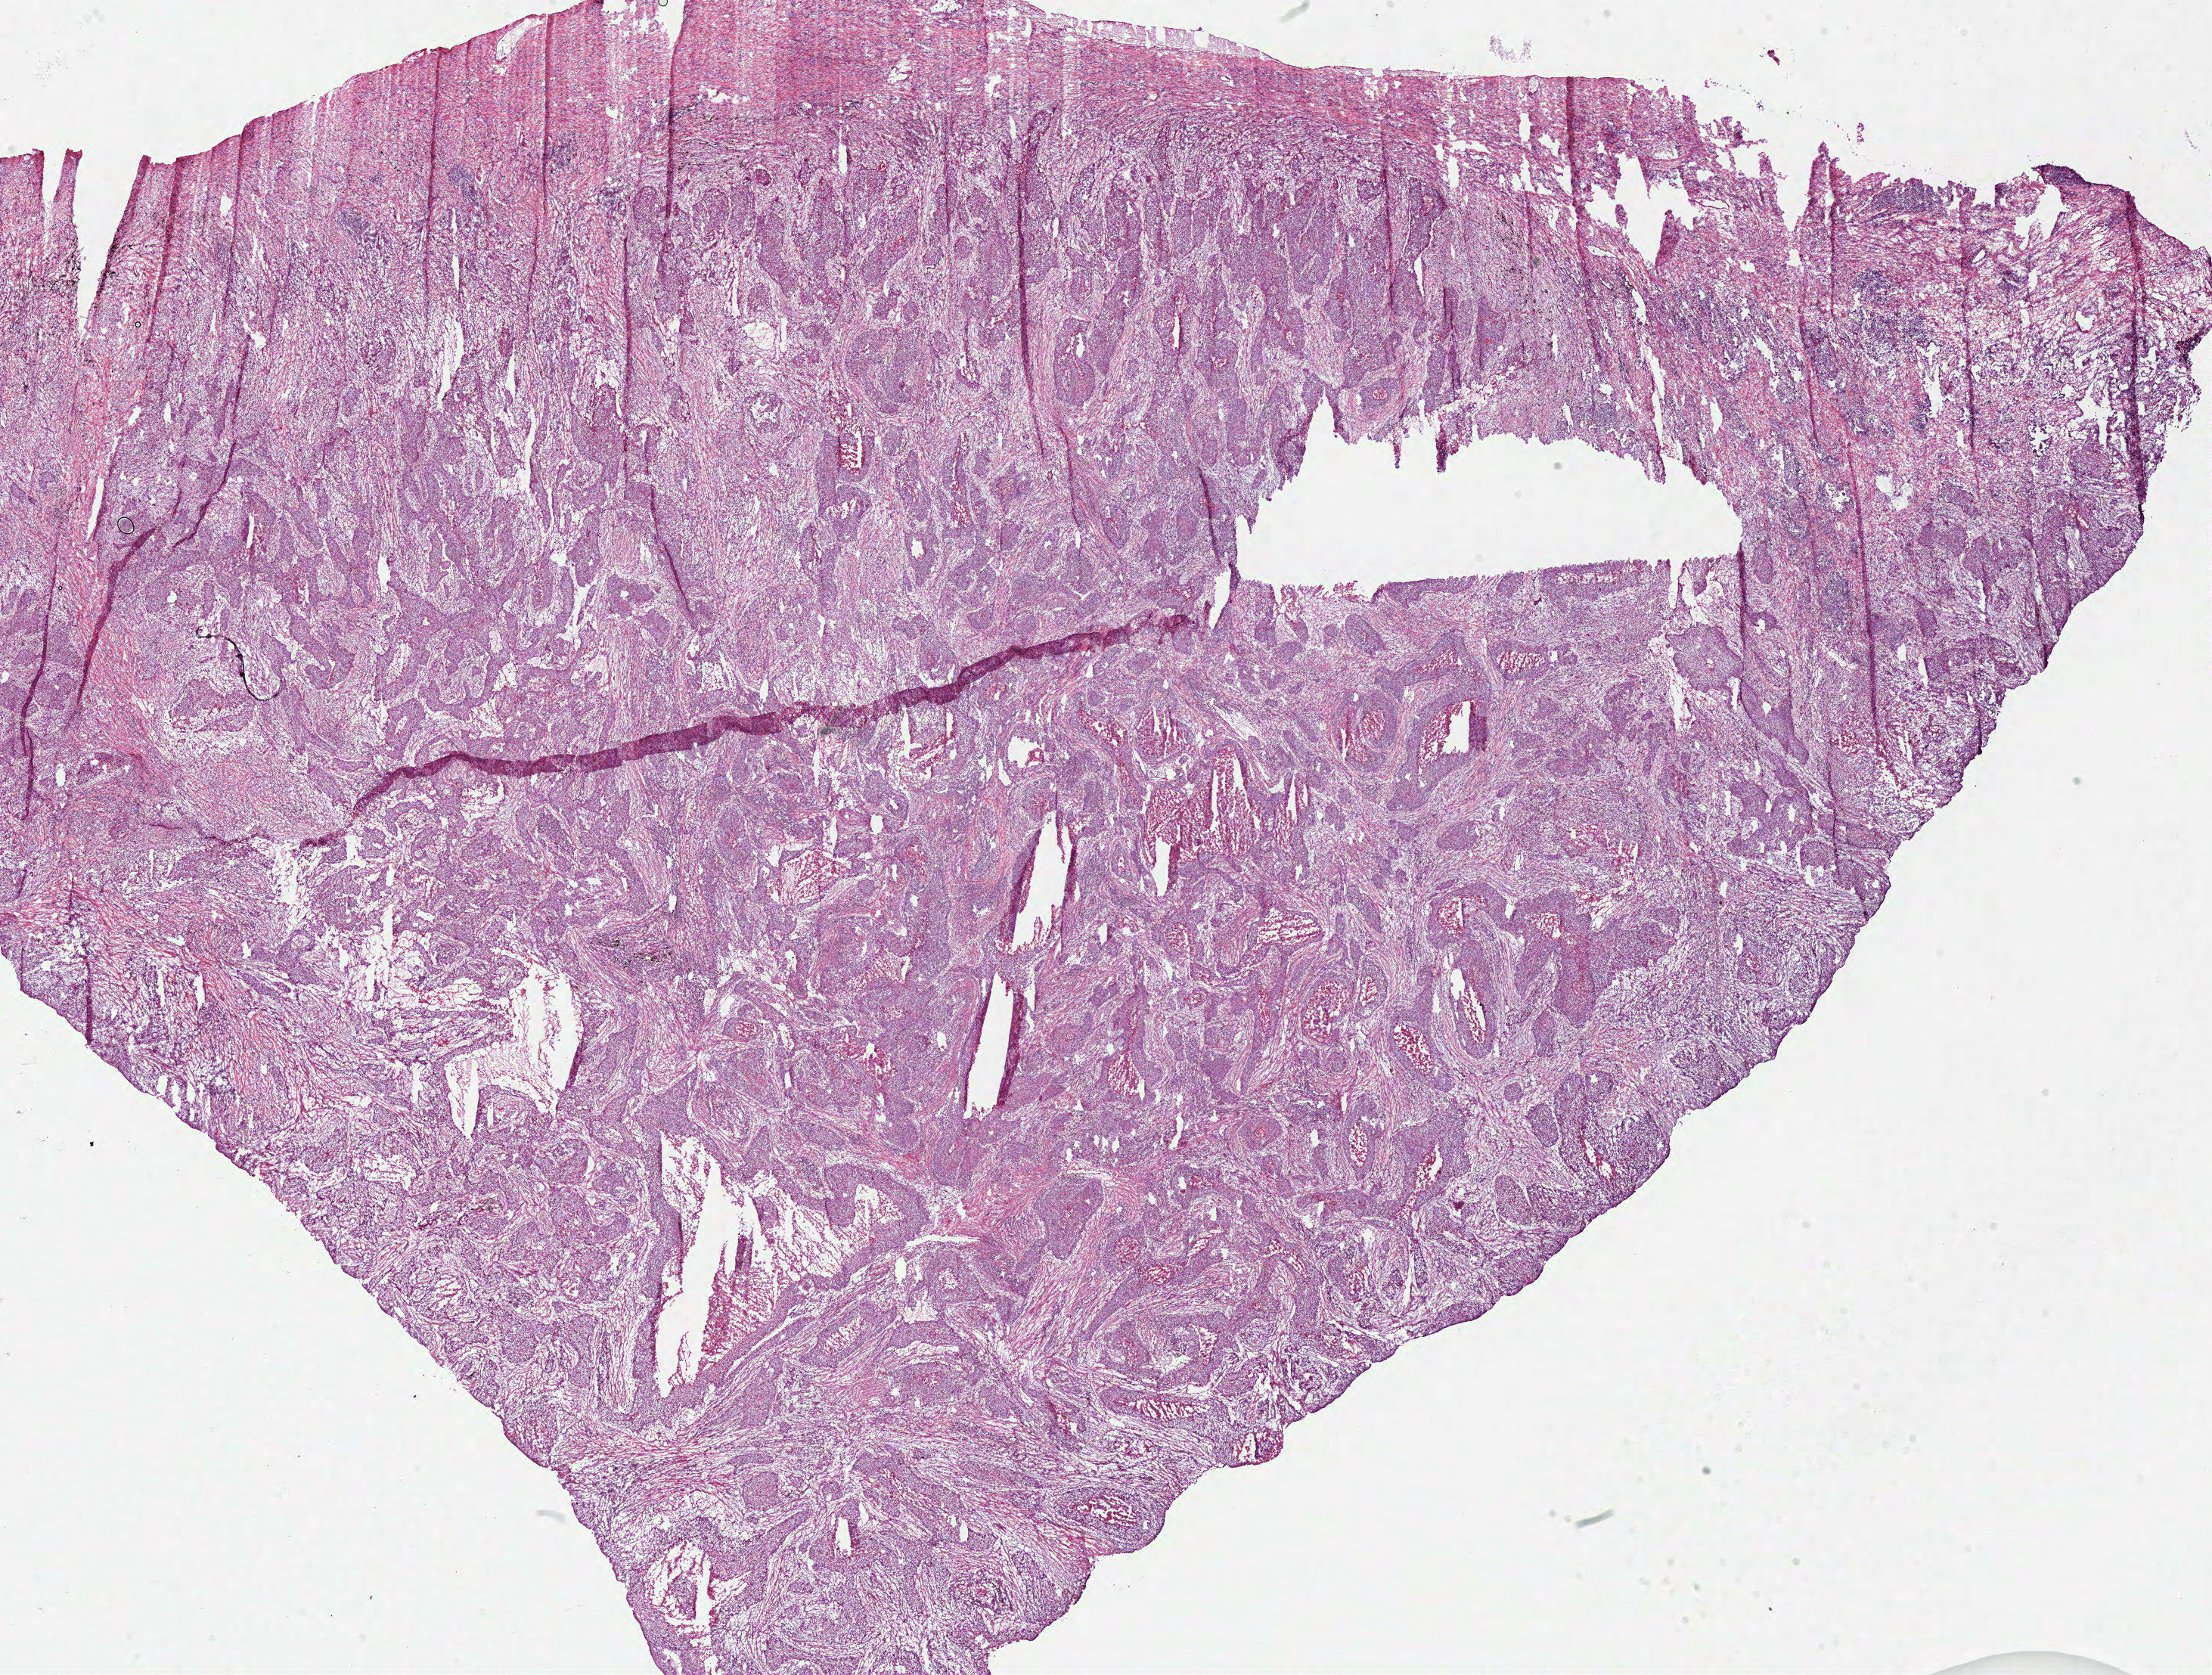
Digitized Hematoxylin and eosin (H&E) stained tissue section (whole slide) — a low-resolution overview of the entire scanned area, about 23.0 x 17.4 mm (slide scanned at 40x); frozen section; primary tumour sample from the lung. Patient: male, age at initial diagnosis 57 years. Slide review estimates, as recorded: tumour cells 70%, tumour nuclei 75%.
Diagnosis: Squamous cell carcinoma, NOS (upper lobe, lung).